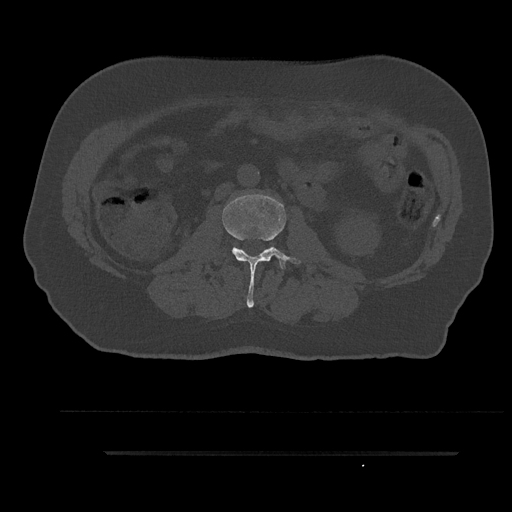
CT including the spine, one axial slice; slice 99 of 797 in the series (ordered by position); reconstruction kernel Br40s/3; 120 kVp; bone window (W 1800 / L 400 HU); 0.5 mm slice thickness; 512 × 512 image matrix, field of view 432 × 432 mm. Male patient, age 63 years. Case-level facts recorded for this patient, not image findings: primary cancer: renal; vertebrae with lytic lesions (as recorded): T8.
Structures marked on this image (semi-automatically segmented with operator editing):
- L2 vertebra: bounding box <222,194,301,308> (left, top, right, bottom; pixels)